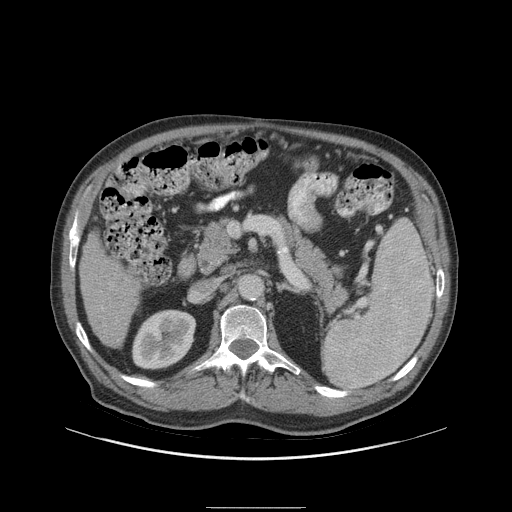
Contrast-enhanced abdominal CT (liver protocol), one axial slice; position 38 of 105 along the scan axis; reconstruction kernel STANDARD; soft-tissue window (W 400 / L 40 HU); 2.5 mm slice thickness; 512 × 512 image matrix, field of view 440 × 440 mm. From the clinical record (not read from this slice): diagnosis: hepatocellular carcinoma (patient treated with transarterial chemoembolisation; whether this scan precedes or follows treatment is not stated here); TNM stage (as recorded): Stage-I; Child-Pugh class: A; tumour size: 5.1 cm.
Outlined on this slice (semi-automatic segmentation, software-assisted and operator-edited):
- liver parenchyma outside the tumour (the mass and vessels are separate outlines, so this box may not span the whole liver): bounding box <78,232,138,348> (left, top, right, bottom; pixels)